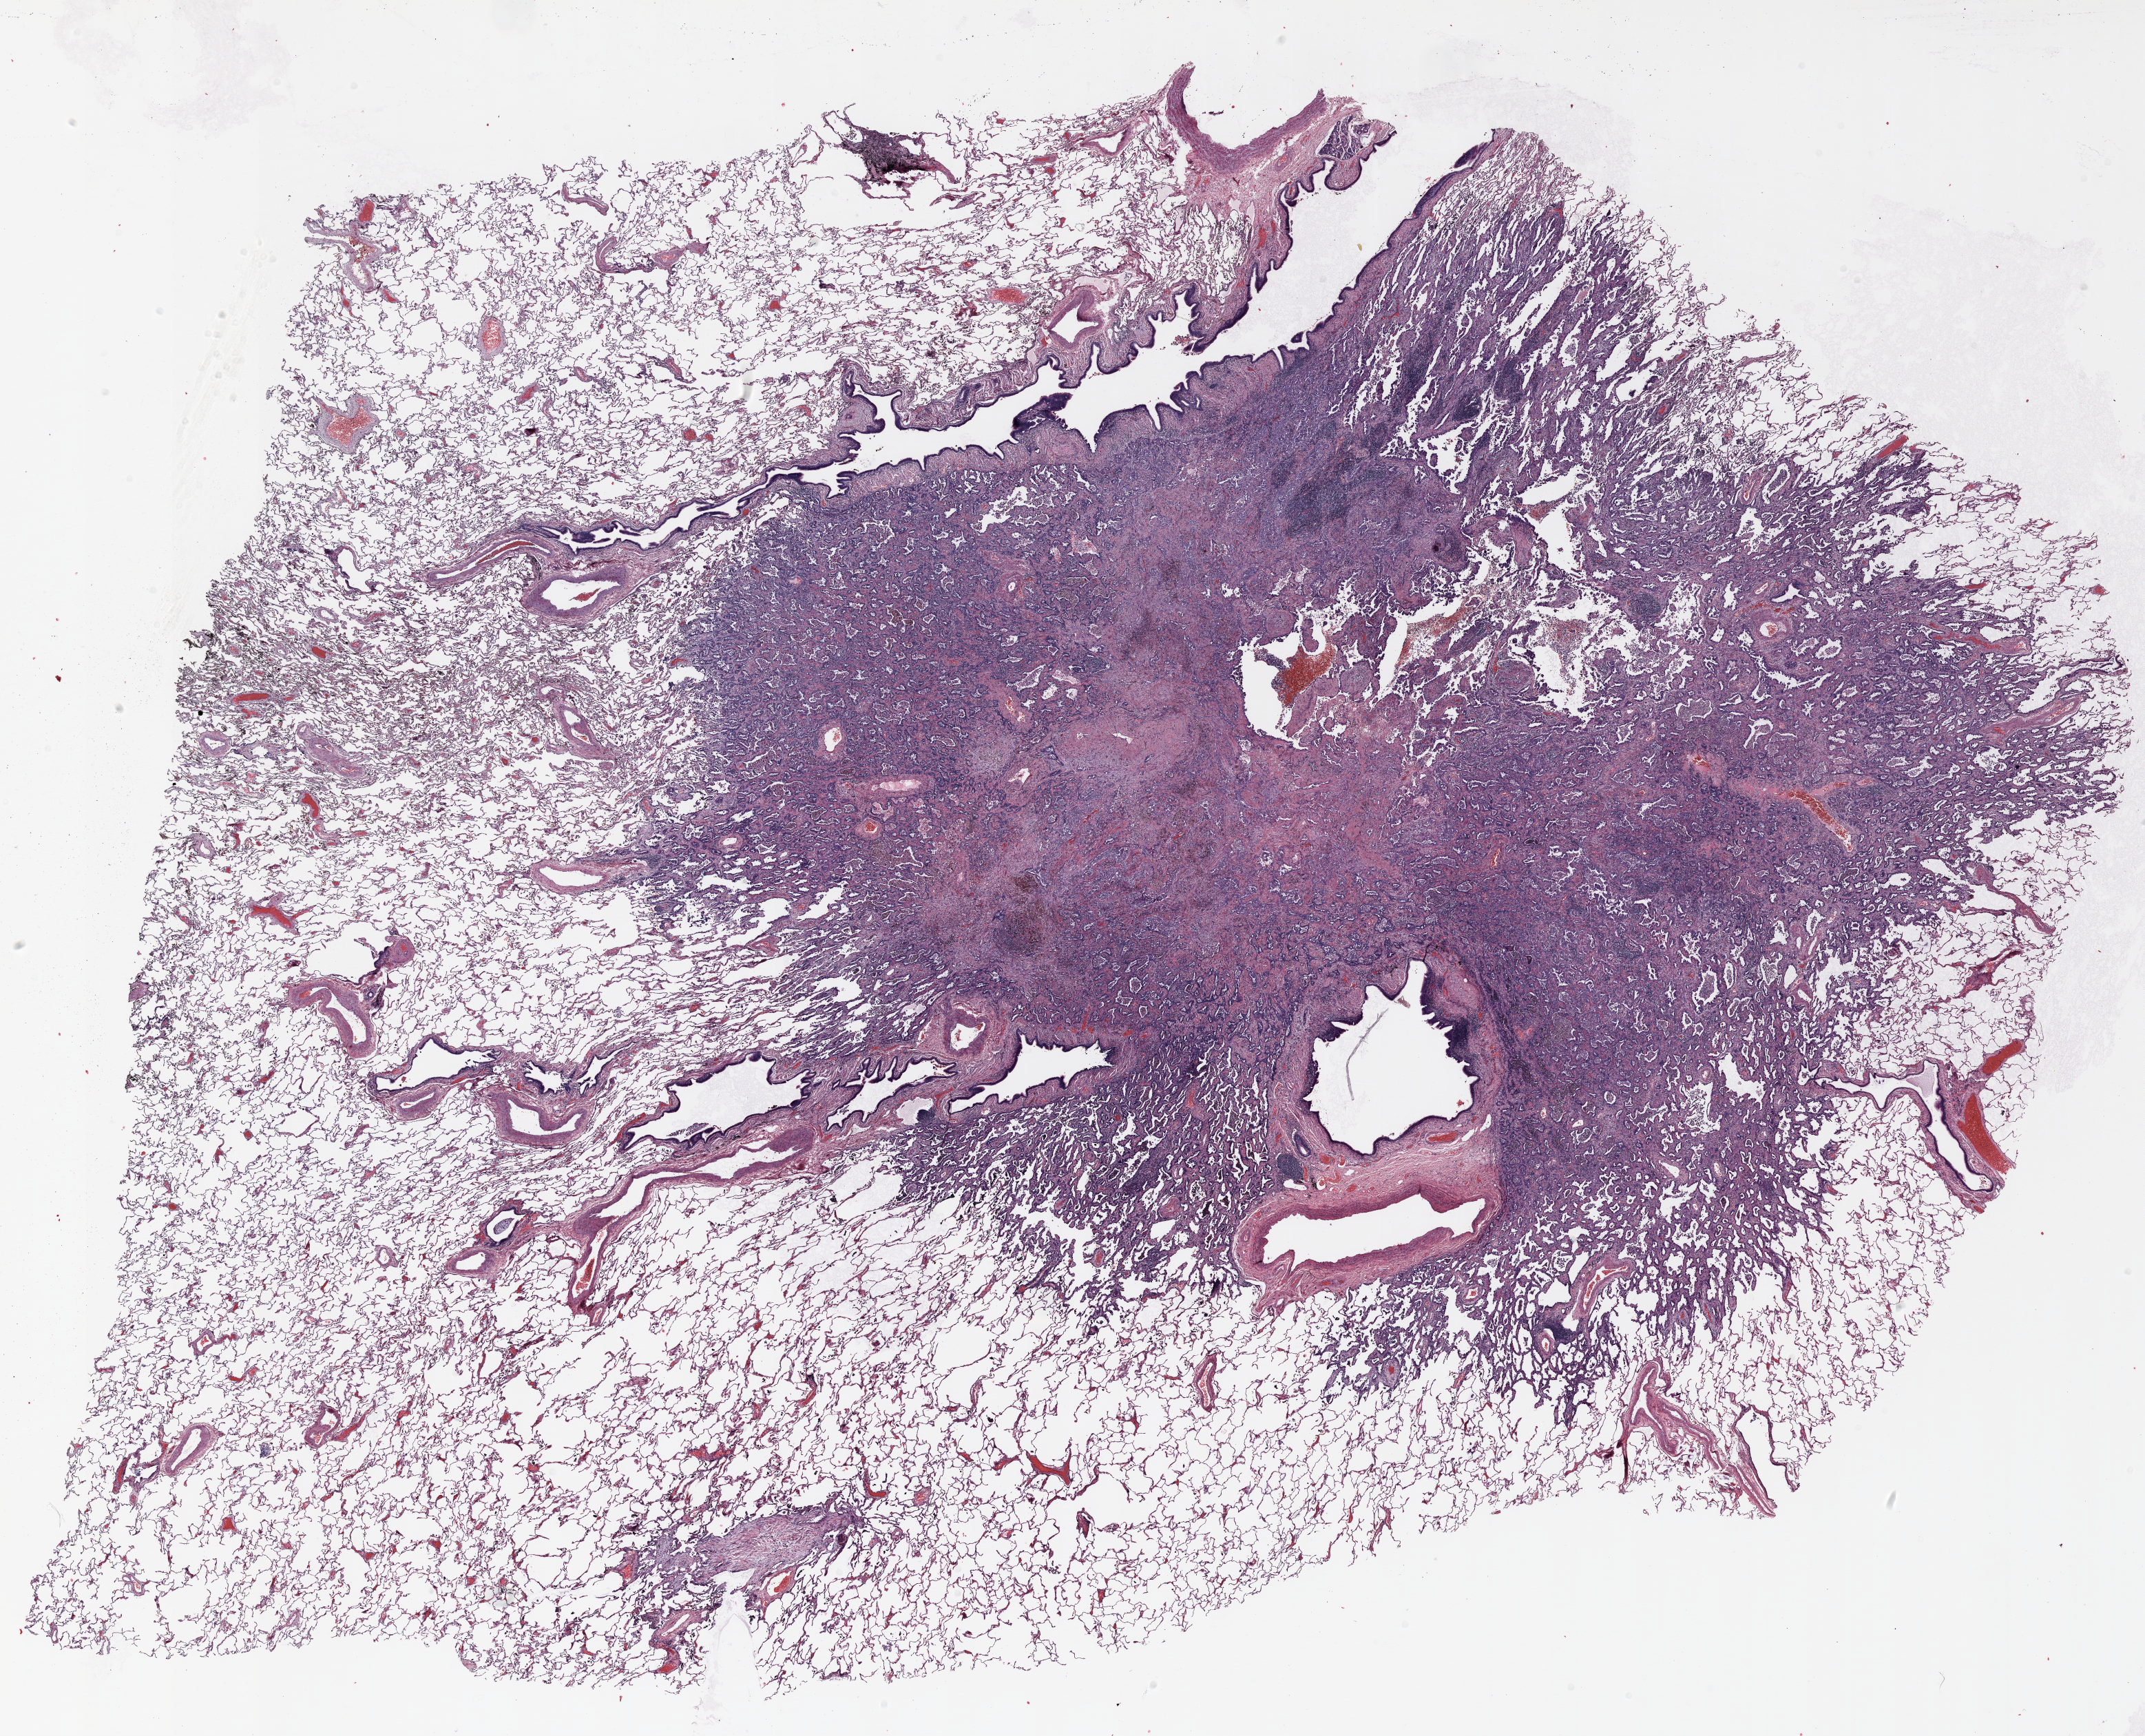
Whole-slide histology image, Hematoxylin and eosin (H&E) stained — a low-resolution overview of the entire scanned area, about 25.0 x 20.3 mm. FFPE section. Lung. Male, age 62 at enrolment. Current smoker at enrolment. Grade: moderately differentiated (G2).
Participant's lung-cancer diagnosis: Adenocarcinoma, NOS. Tumour size (pathology): 30 mm. Stage (AJCC 6th edition): IA. Primary tumour location (clinical record): left lower lobe.